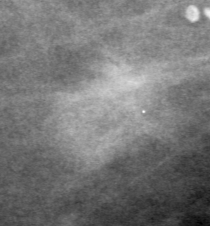
Cropped region of a digitized screen-film mammogram centred on a radiologist-marked abnormality, left breast, CC view, BI-RADS breast density category 1 (scale 1–4).
Finding: mass, shape lobulated, margins obscured; BI-RADS assessment category 0 (incomplete: needs additional imaging); pathology (as recorded): malignant.